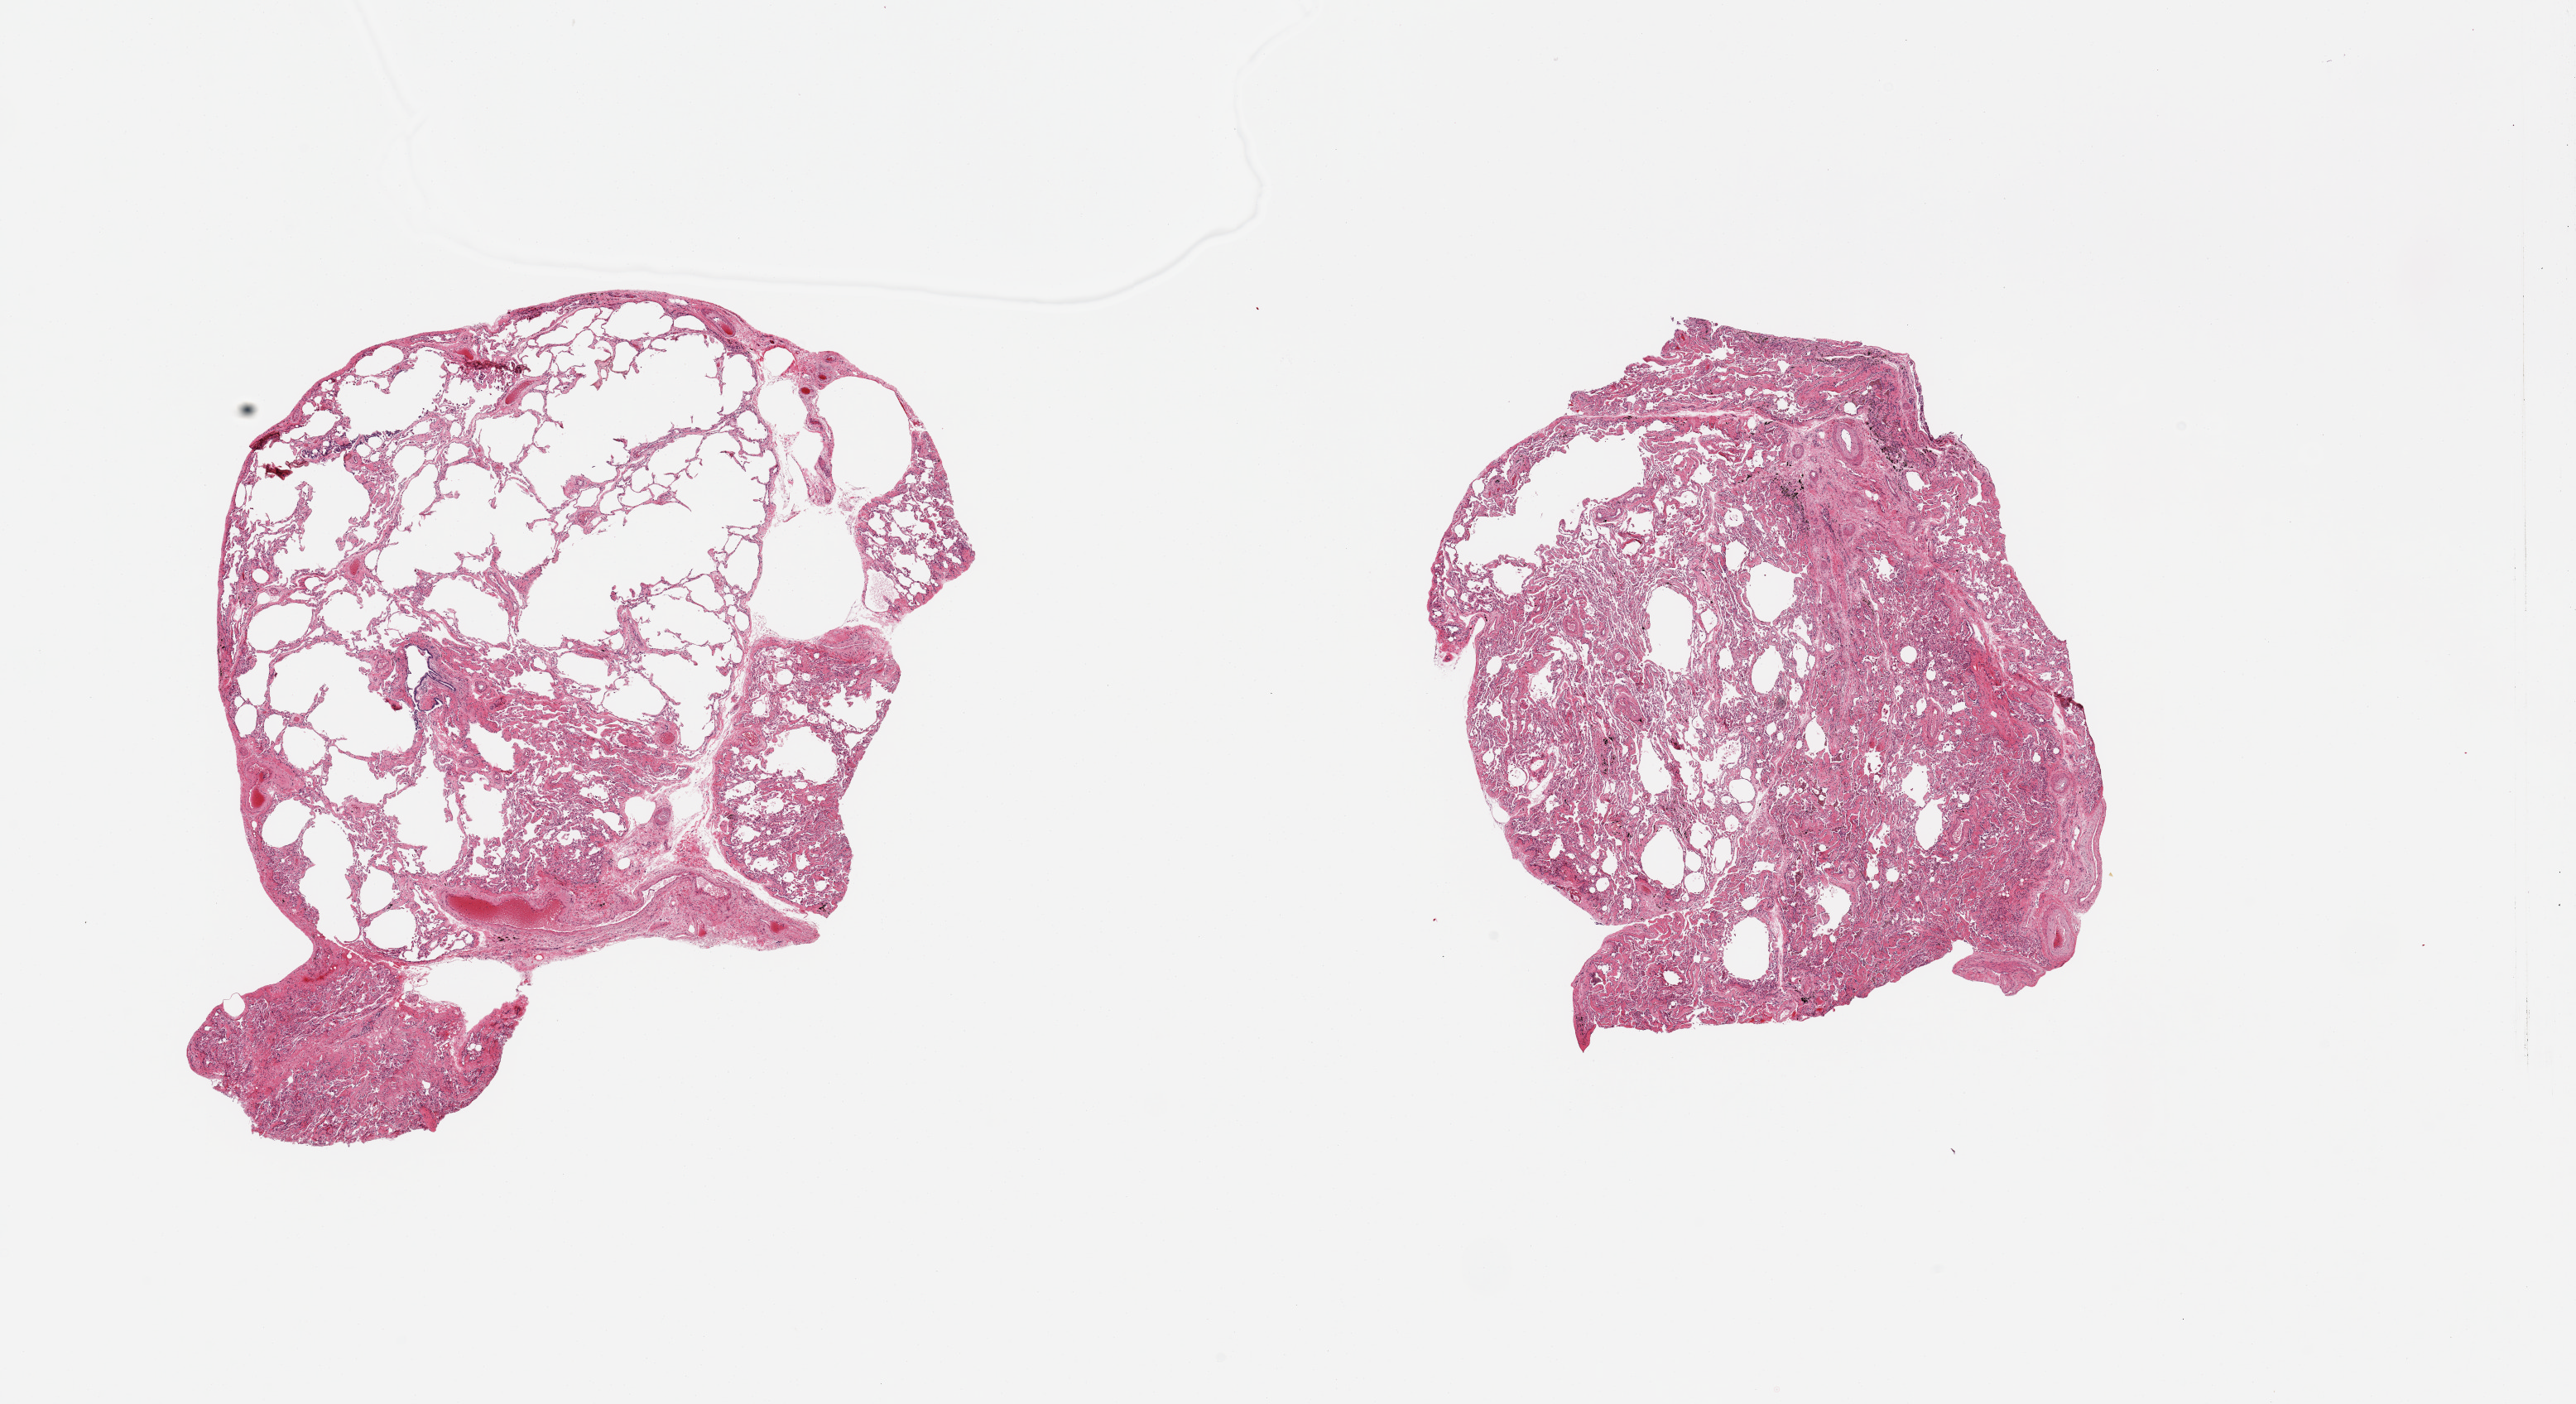
Hematoxylin and eosin (H&E) whole-slide image — shown as a low-resolution overview of the whole scanned area (about 24.6 x 13.4 mm). PAXgene-fixed, paraffin-embedded tissue. Sampled site (target tissue): lung. Donor tissue sample. Donor sex: female.
* pathologist's review note for this sample: 2 pieces, emphysematous changes, moderate congestion